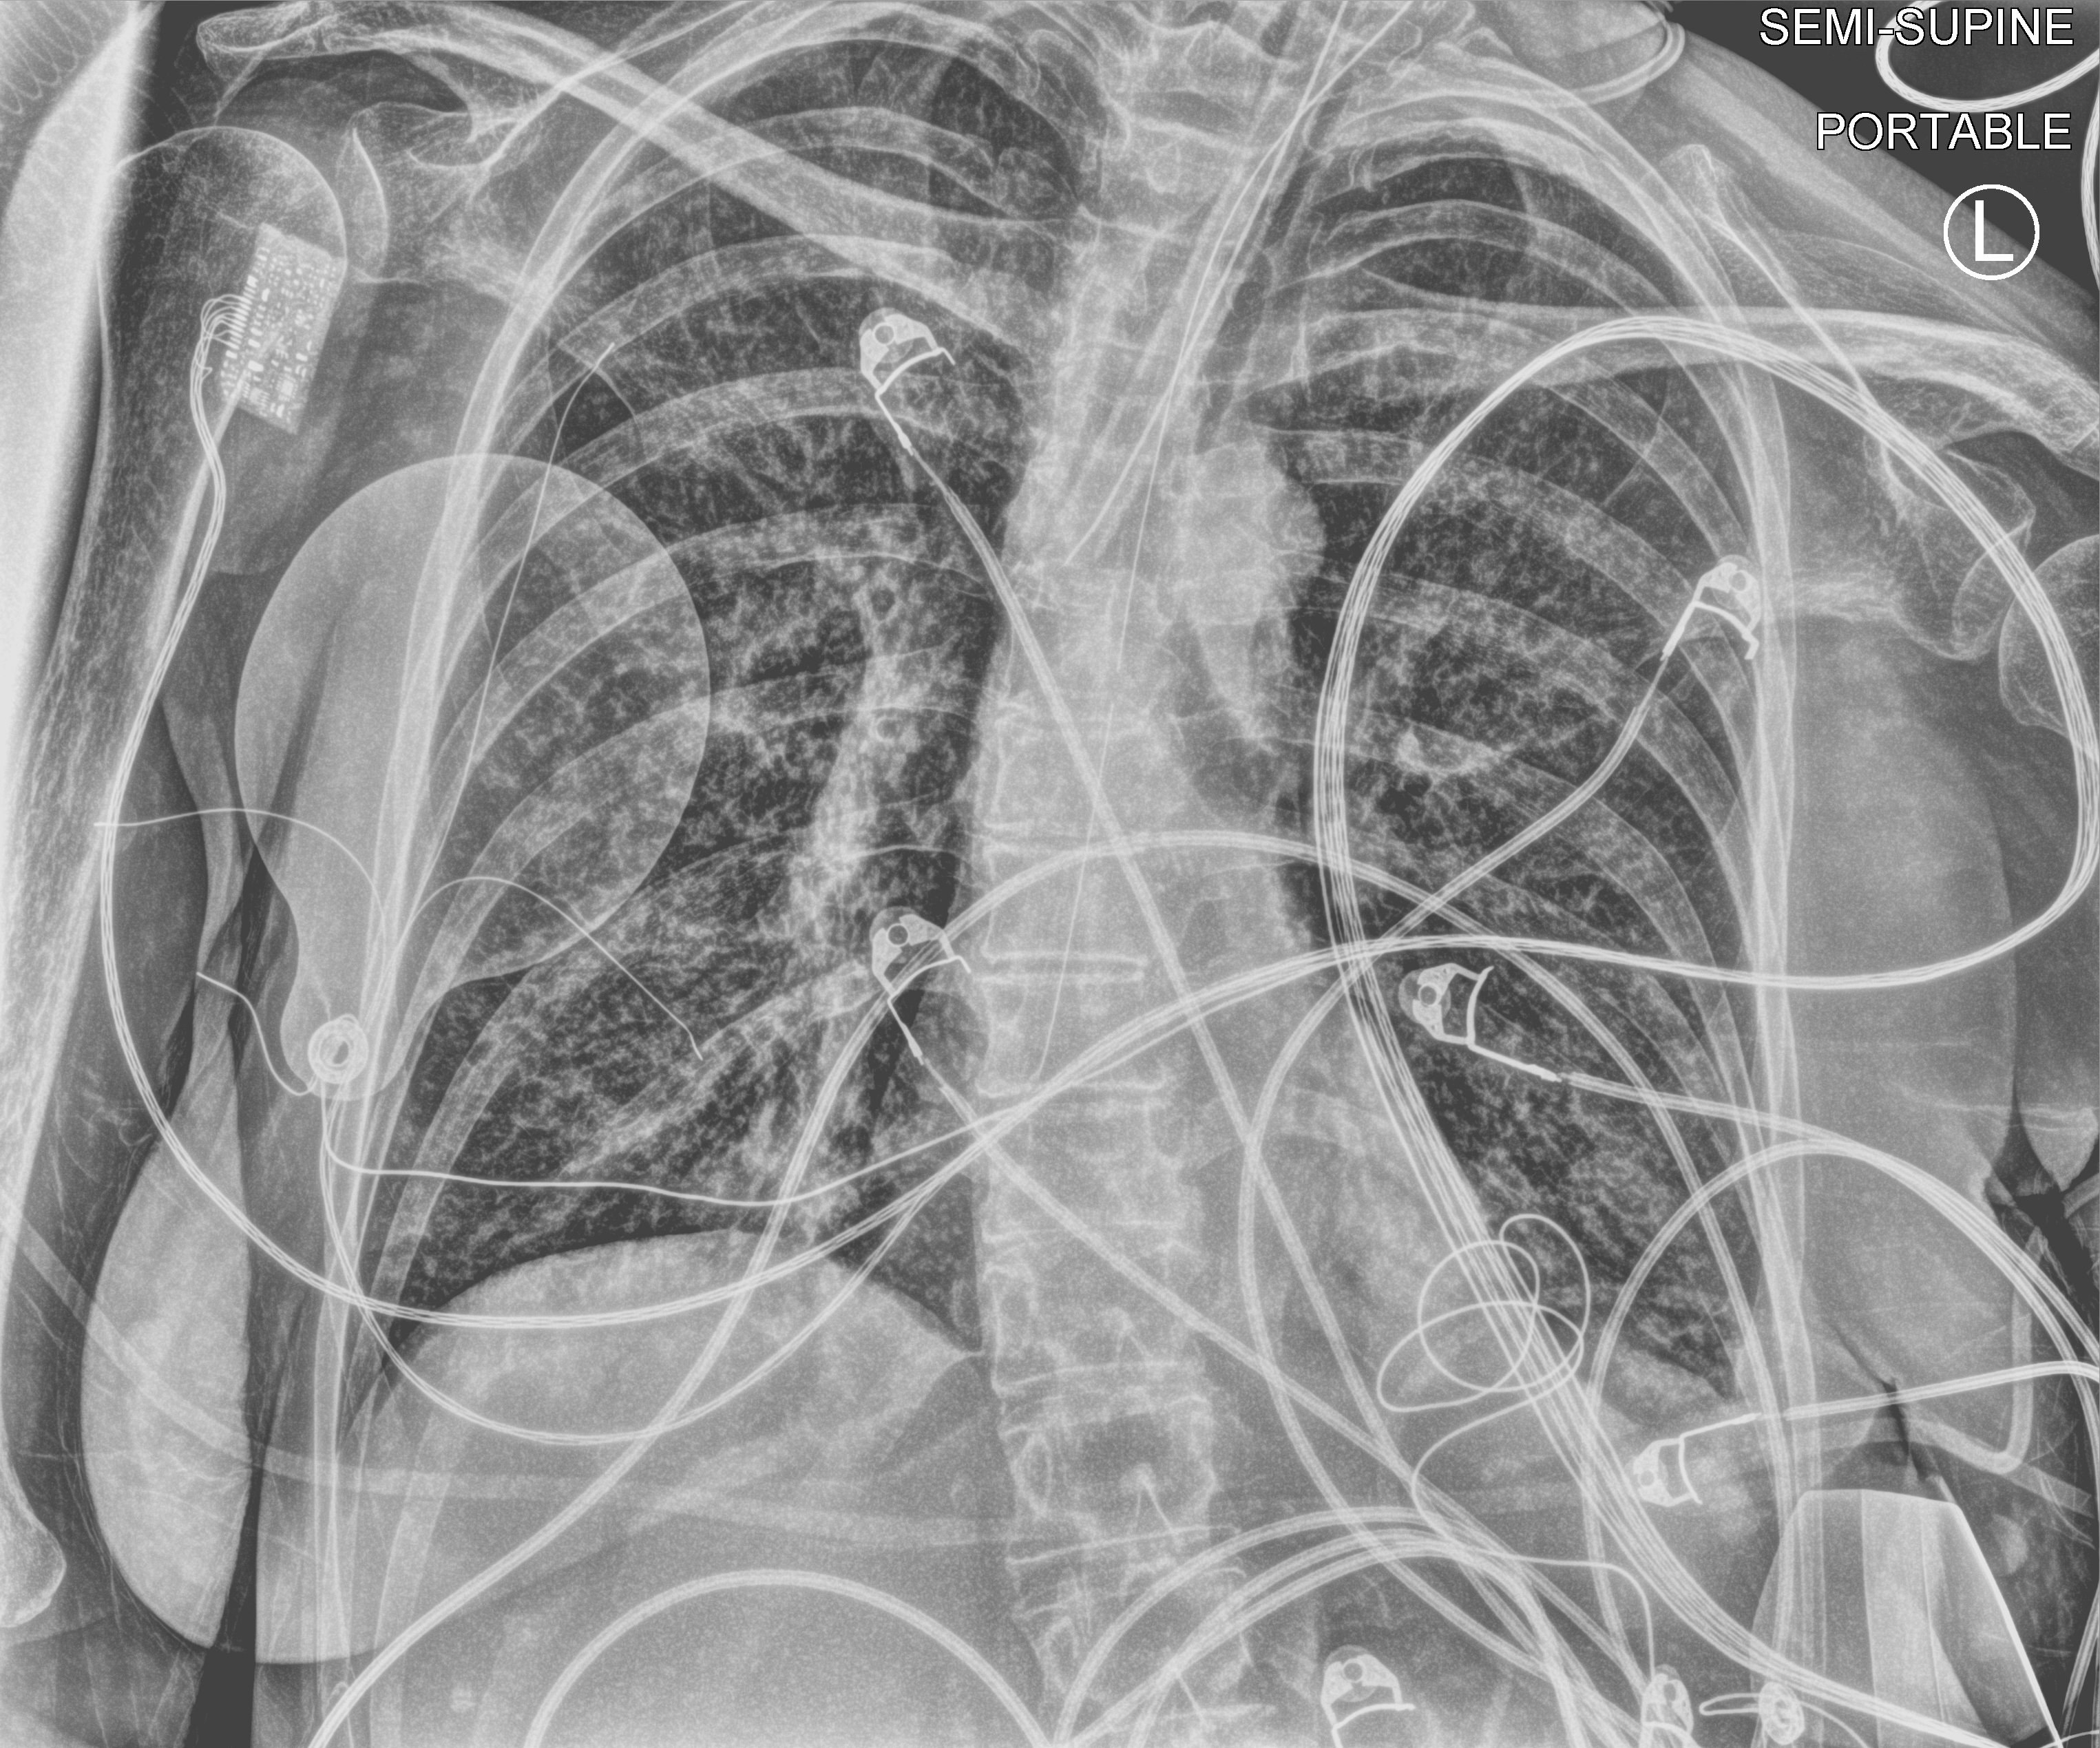
Portable chest radiograph, anteroposterior (AP) projection. Adult patient hospitalised with COVID-19, age 18–59 years.
Hospital-stay facts (about this admission, not read from this image; timing relative to this image not recorded): admitted to intensive care during this hospital stay: yes.